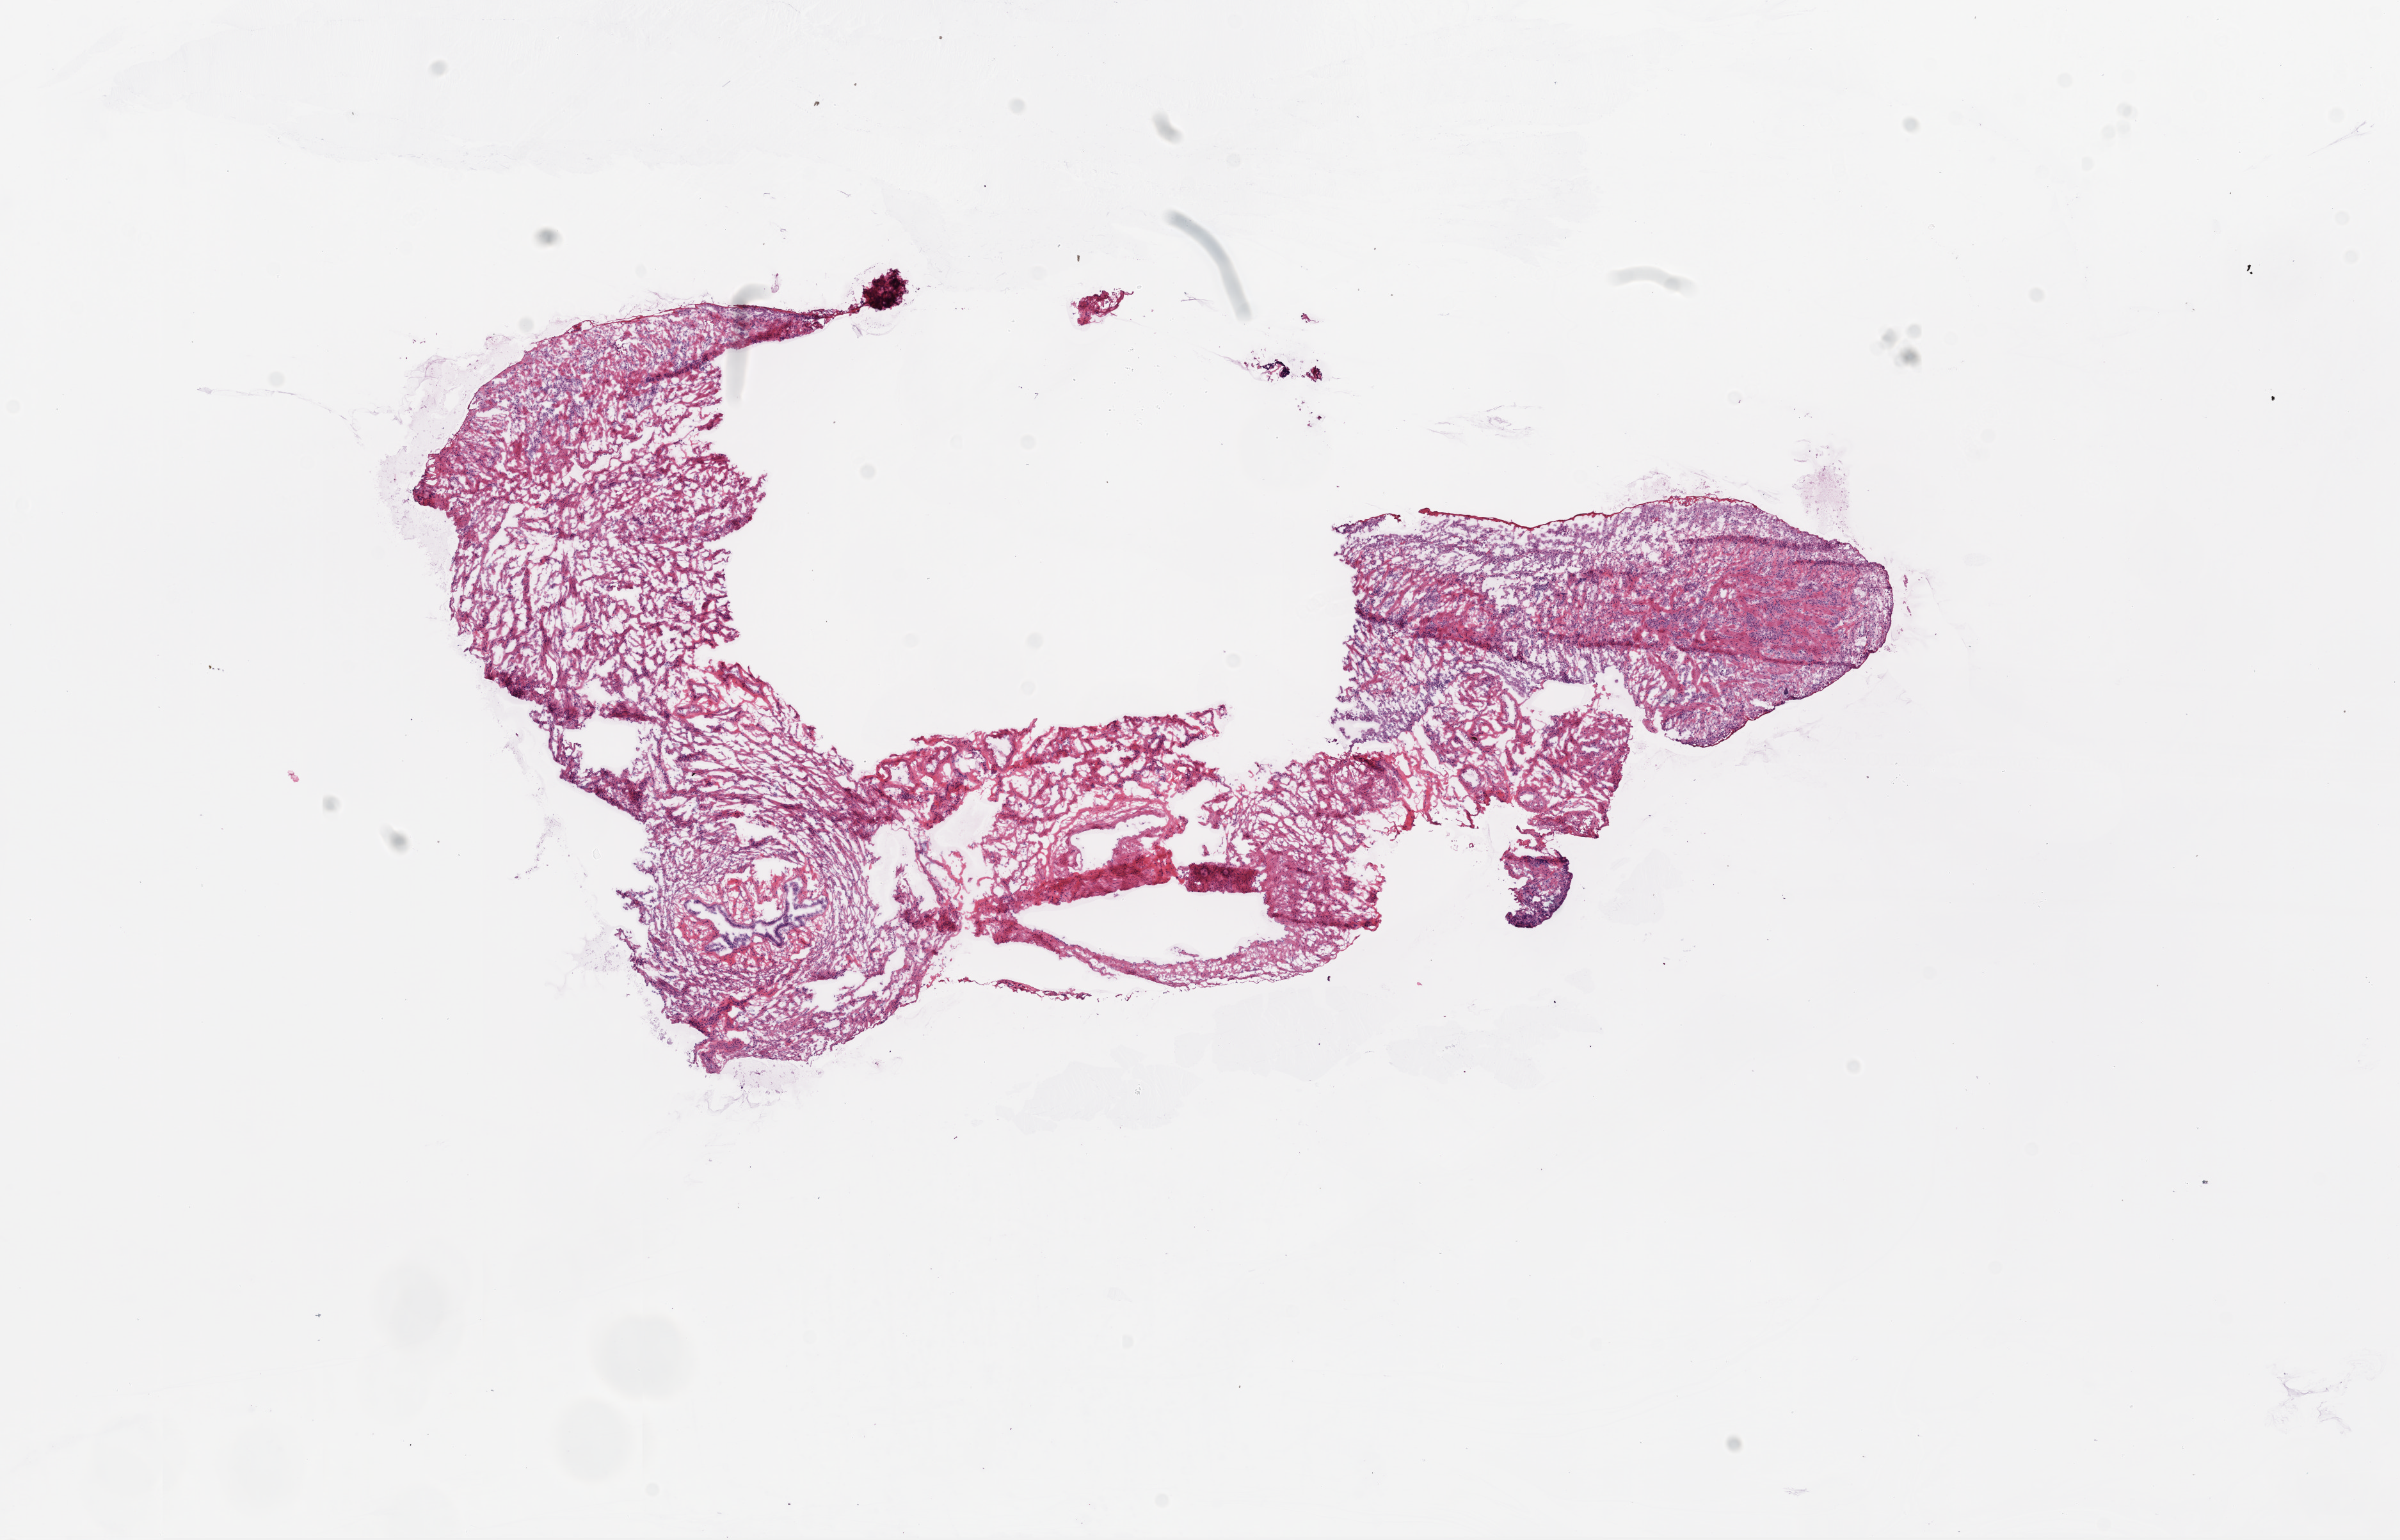
Digitized H&E tissue section (whole slide), low-resolution overview of the scanned area, about 15.0 x 9.7 mm (acquisition: 20x scan). Frozen section from the bottom of the tissue portion. Ovary, solid tissue normal (non-tumour tissue) sample. Patient: female, age at initial diagnosis 51 years.
This section: solid tissue normal sample (biorepository sample class). Patient diagnosis: Serous cystadenocarcinoma, NOS.